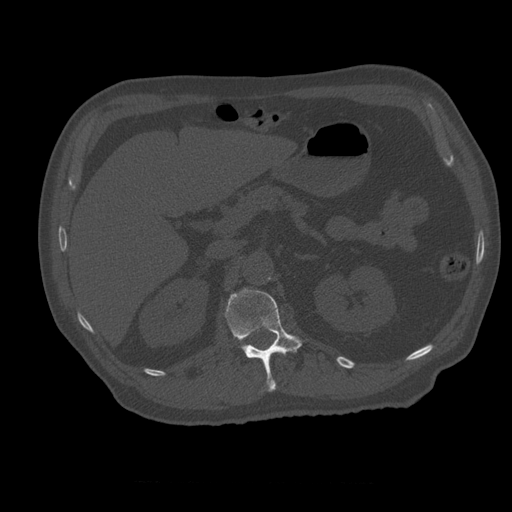
CT including the spine, one axial slice. Slice 238 of 399 in the series (ordered by position). Reconstruction kernel STANDARD. Bone window (W 1800 / L 400 HU). 1.25 mm slice thickness. 512 × 512 image matrix, field of view 407 × 407 mm. Patient age 73 years. From the clinical record (not read from this slice): primary cancer: prostate; vertebrae with lytic lesions (as recorded): L2.
Annotated regions visible in this slice (semi-automatic segmentation, software-assisted and operator-edited):
- L1 vertebra: bounding box <225,289,302,392> (left, top, right, bottom; pixels)